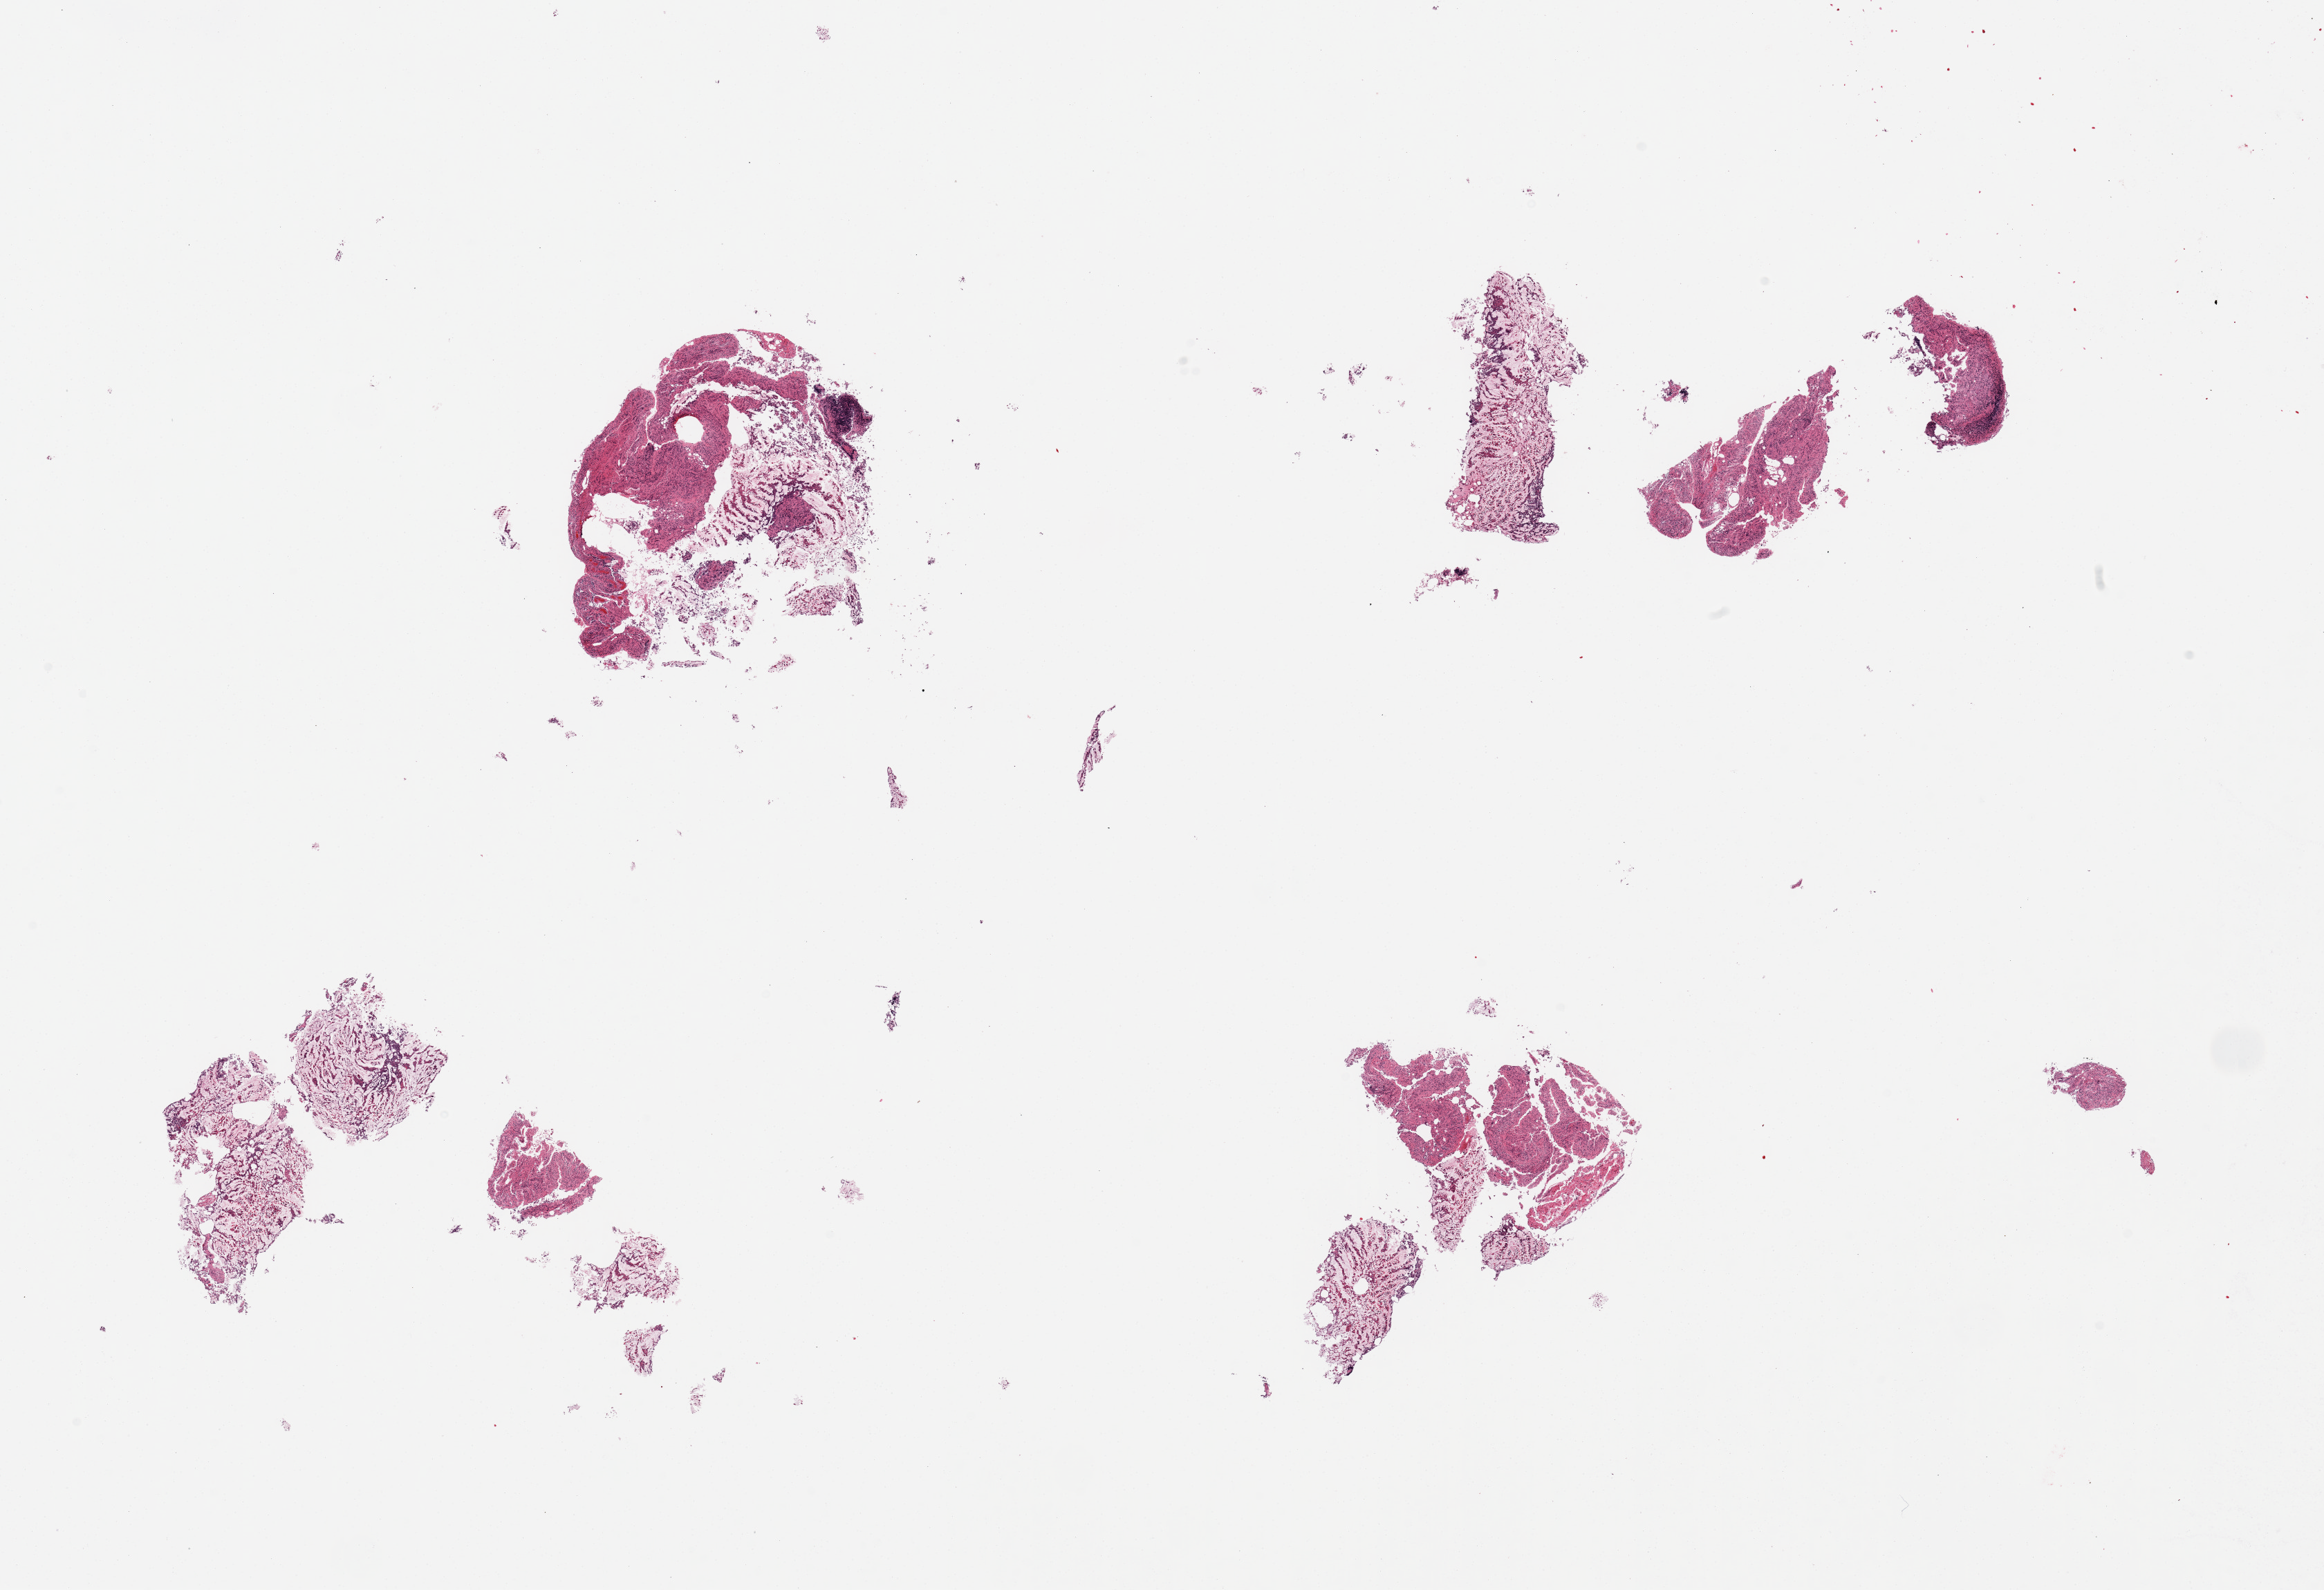
H&E whole-slide image, brightfield — a low-resolution overview of the entire scanned area, about 26.6 x 18.2 mm. PAXgene-fixed paraffin-embedded (PFPE) section. Sampled site (target tissue): ileum. Donor tissue sample. Donor sex: male.
Reviewer comment on this tissue sample: 4 pieces (fragmented); autolyzed with minimal lymphoid tissue.